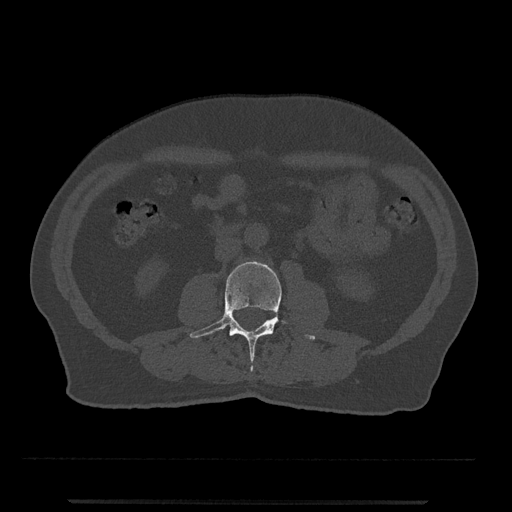
CT including the spine, one axial slice. Position 201 of 797 along the scan axis. 120 kVp. Bone window (W 1800 / L 400 HU). 512 × 512 image matrix, field of view 419 × 419 mm. Male patient, age 63 years. From the clinical record (not read from this slice): primary cancer: prostate.
Annotated regions visible in this slice (semi-automatic segmentation, software-assisted and operator-edited):
- L3 vertebra: bounding box [x1, y1, x2, y2] px = [189, 261, 315, 371]